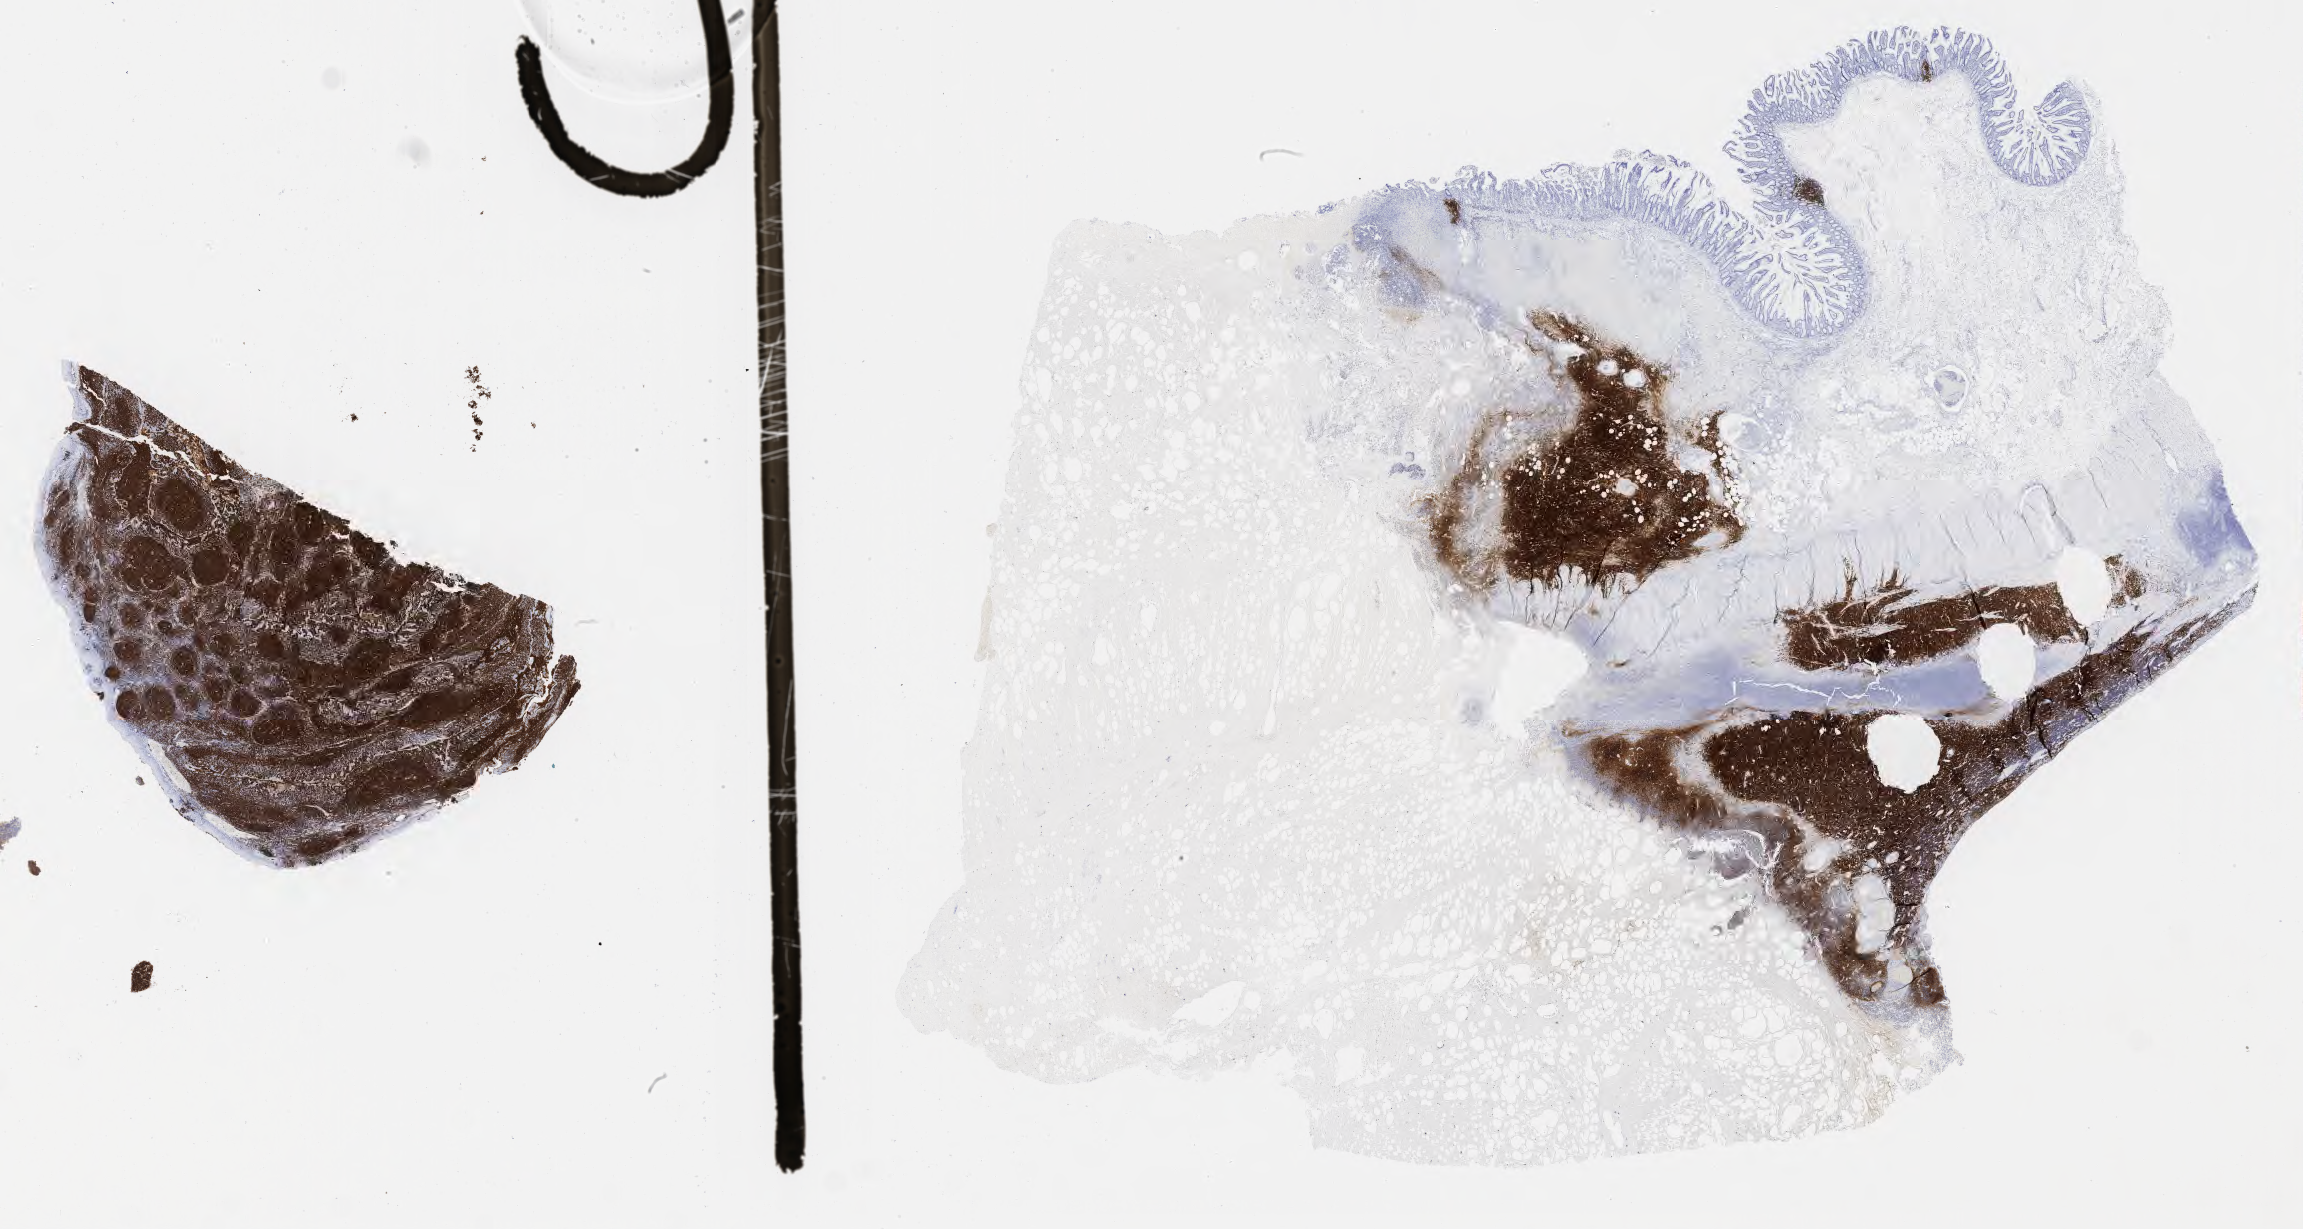
Immunohistochemistry (IHC) whole-slide image stained for CD20, a low-resolution overview of the entire scanned area, about 37.2 x 19.9 mm; tumor tissue; site: colon. Patient: male, aged 62.
Histologic diagnosis: Burkitt lymphoma, NOS.